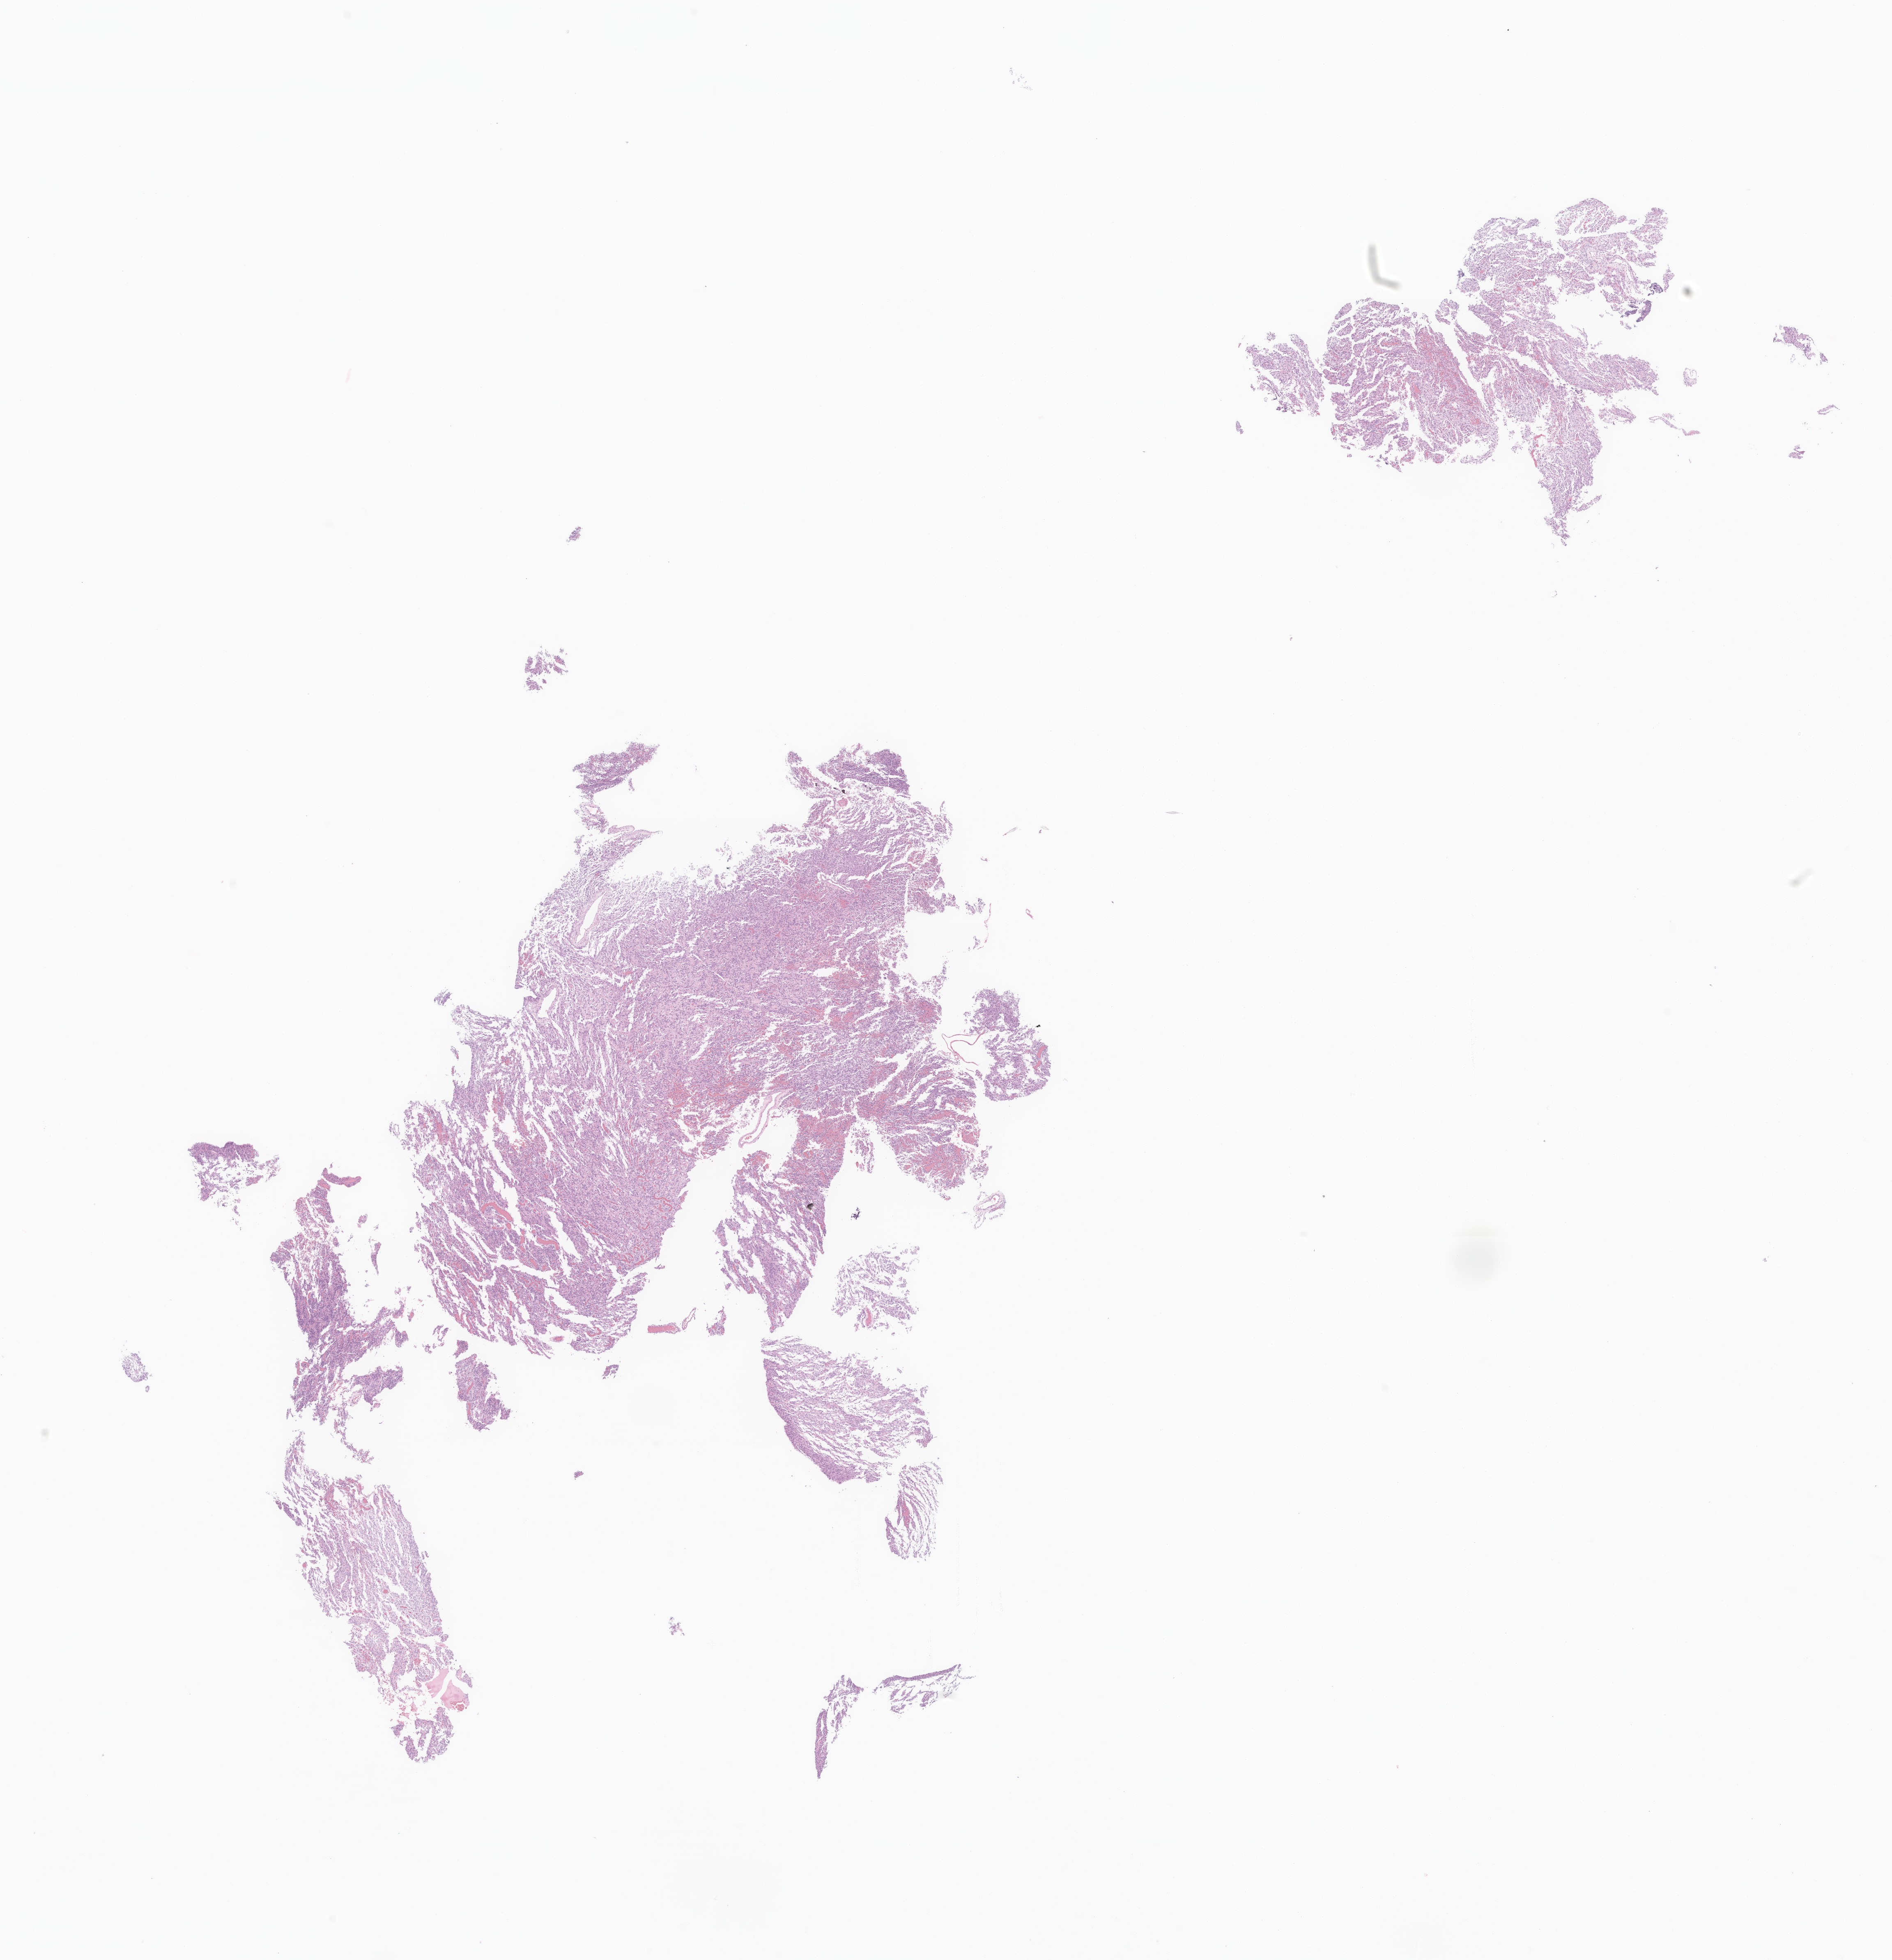
Digitized haematoxylin and eosin-stained section of tumor tissue from the brain, a low-resolution overview of the entire scanned area, about 19.4 x 20.1 mm, FFPE section. Female patient, age 165 months (13 years 9 months).
Recorded diagnosis: Pleomorphic xanthoastrocytoma, NOS.